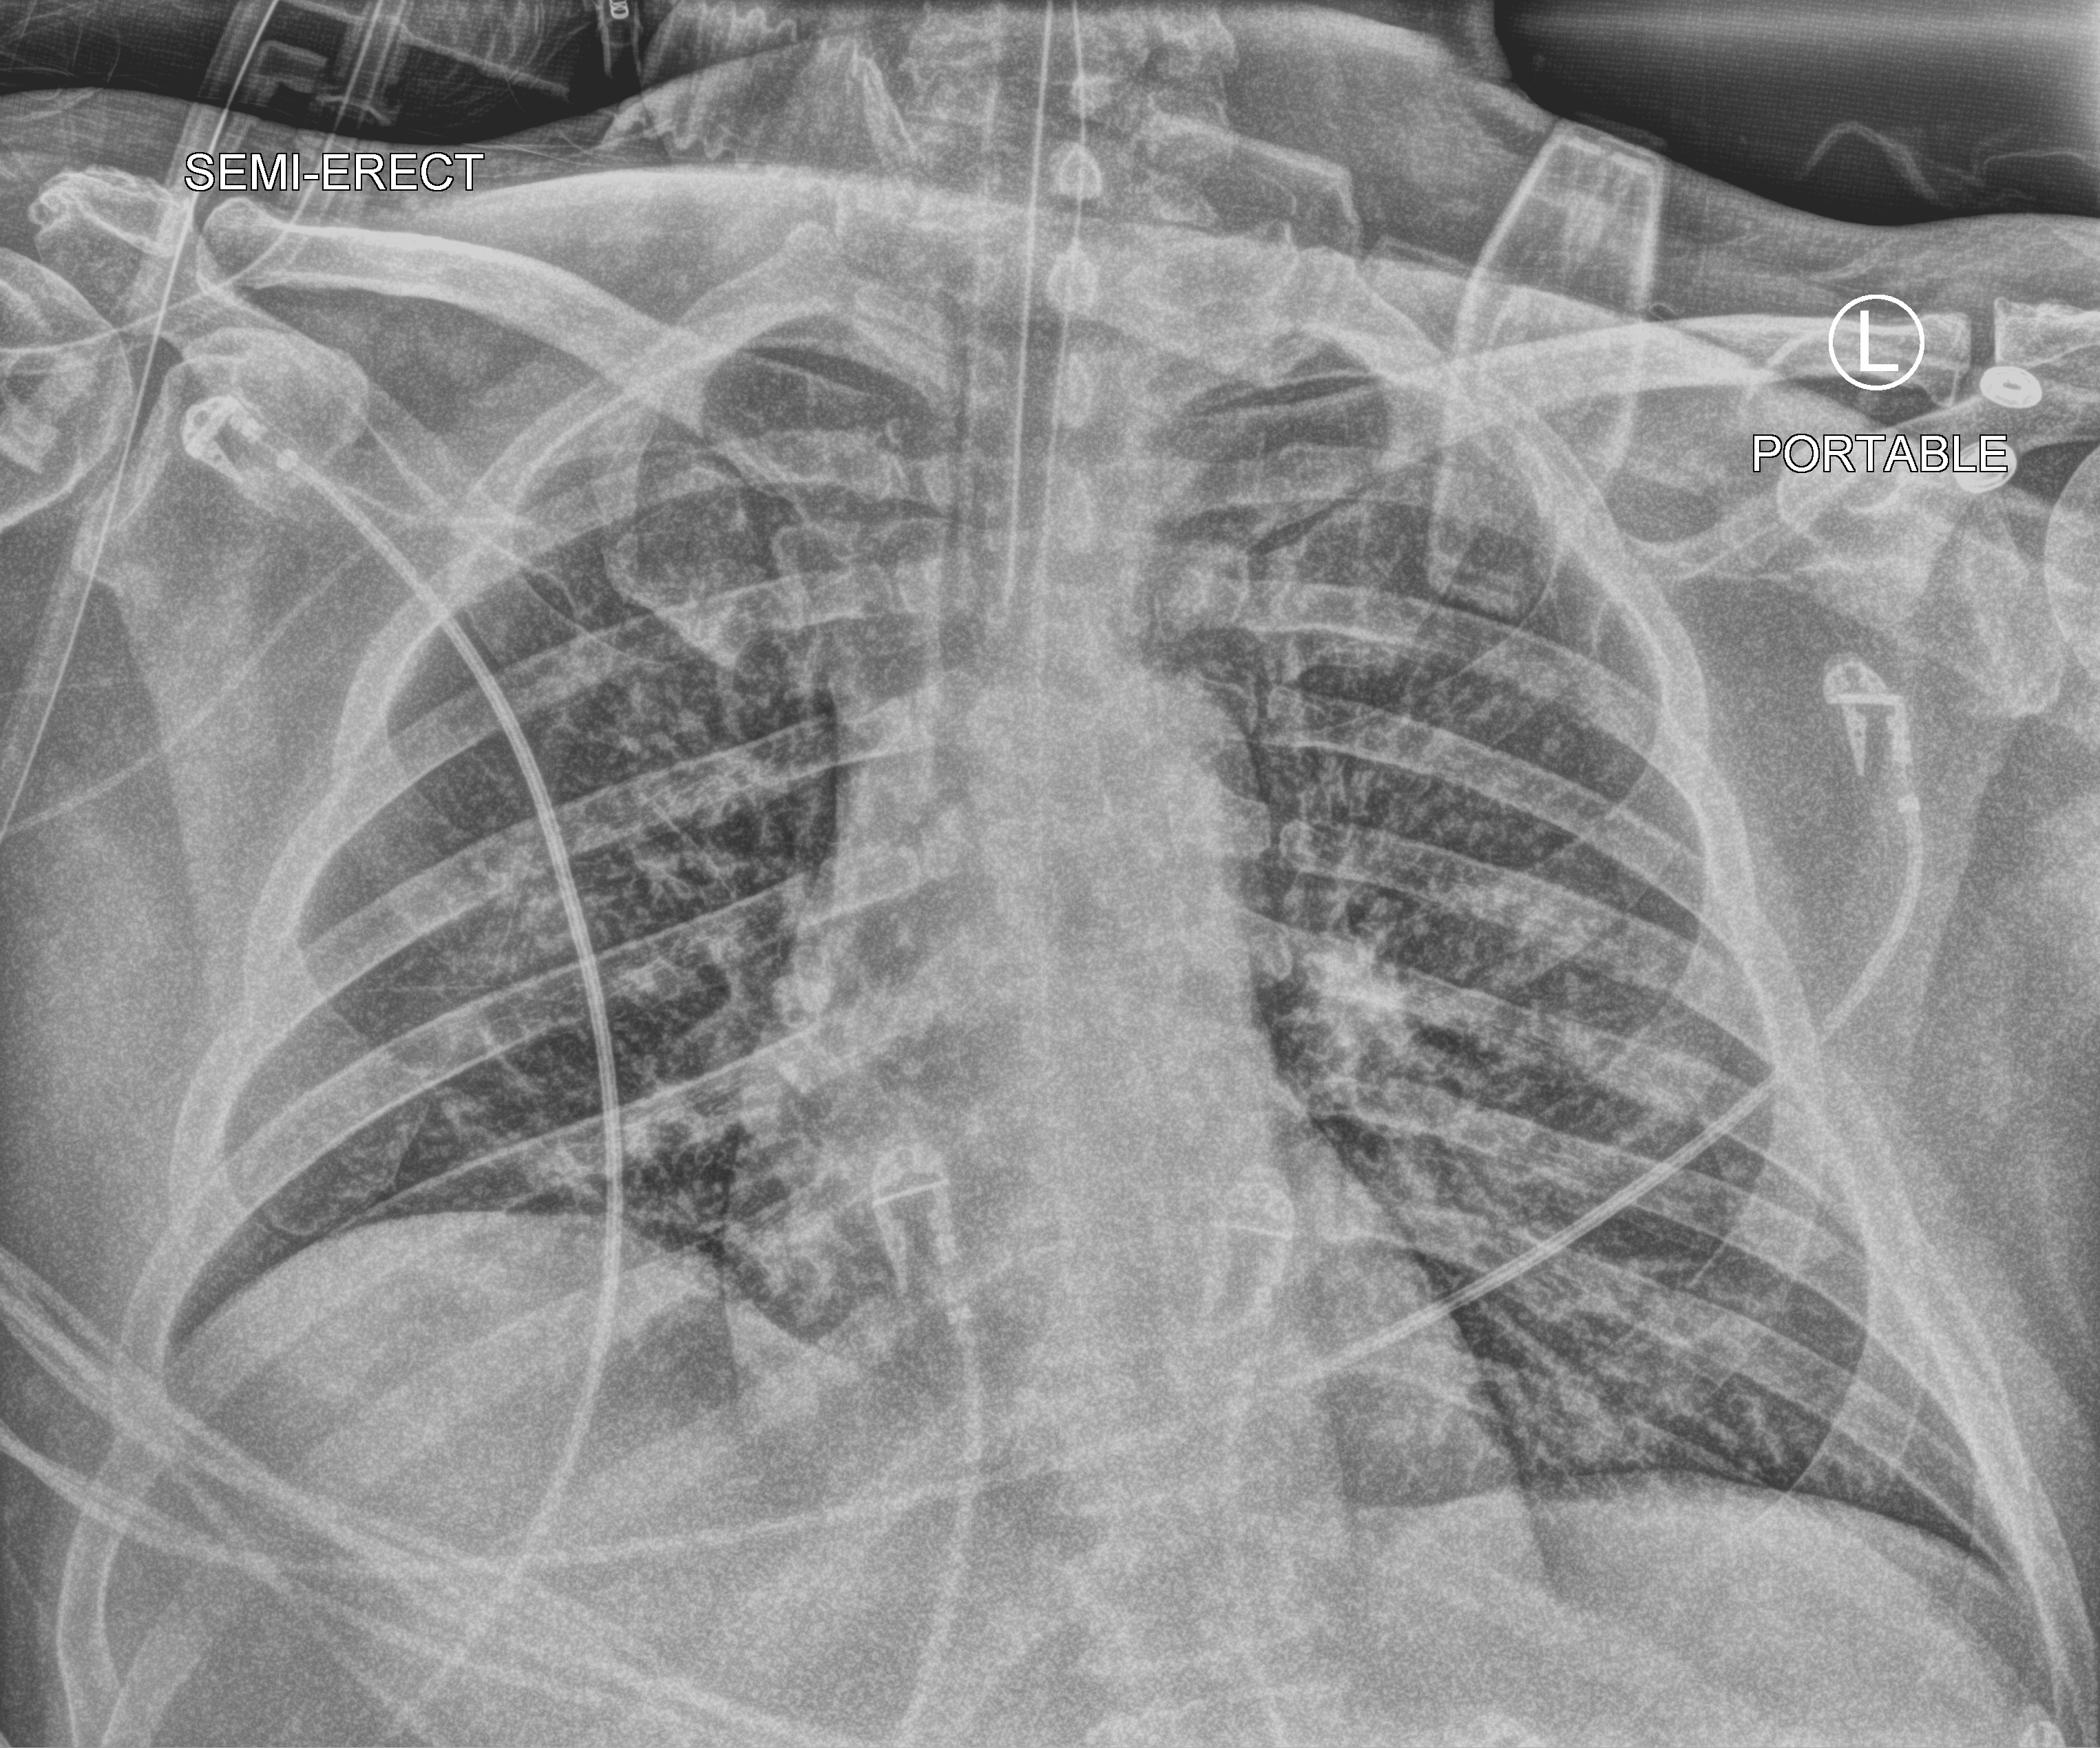
Portable chest radiograph, anteroposterior (AP) projection. Male patient hospitalised with COVID-19, age 18–59 years.
From the hospital-stay record, not from the radiograph (when in the stay this image was taken is not recorded):
- admitted to intensive care during this hospital stay: yes